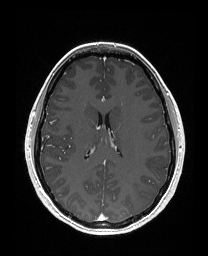
Brain MRI from a brain-tumour surgery series, one axial slice; slice 97 of 176 in the series (ordered by position); T1-weighted post-contrast; 1 mm slice thickness; 208 × 256 image matrix, field of view 203 × 250 mm. From the clinical record (not read from this slice): histopathology: Astrocytoma; WHO grade: 3; IDH mutation: yes; tumour location: Left Frontal.
Outlined on this slice (manually delineated by an expert):
- tumour: bounding box [x1, y1, x2, y2] px = [142, 132, 149, 139]